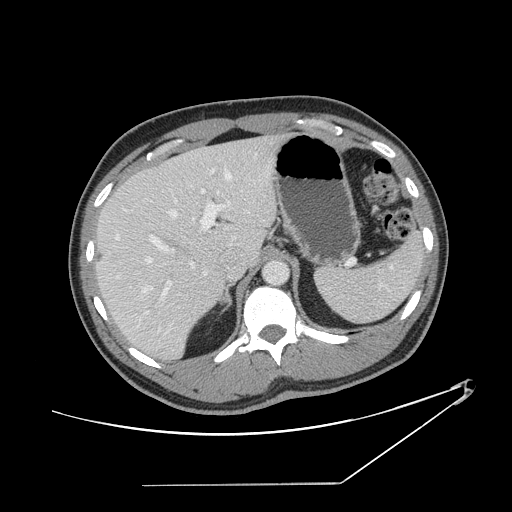
Contrast-enhanced abdominal CT, one axial slice. Reconstruction kernel STANDARD. 120 kVp. Intravenous contrast given. Soft-tissue window (W 400 / L 40 HU). 512 × 512 image matrix. Male patient, age 45 years. From the clinical record (not read from this slice): diagnosis: colorectal cancer liver metastases, imaged before liver resection; multiple liver metastases: no.
Annotated regions visible in this slice (expert manual segmentation):
- hepatic veins: bounding box (x1, y1, x2, y2) in pixels: (113, 155, 256, 293)
- liver: (98, 137, 281, 358)
- planned liver remnant (the part of the liver to remain after resection): (98, 154, 231, 358)
- portal vein (with intrahepatic branches): (136, 170, 225, 333)